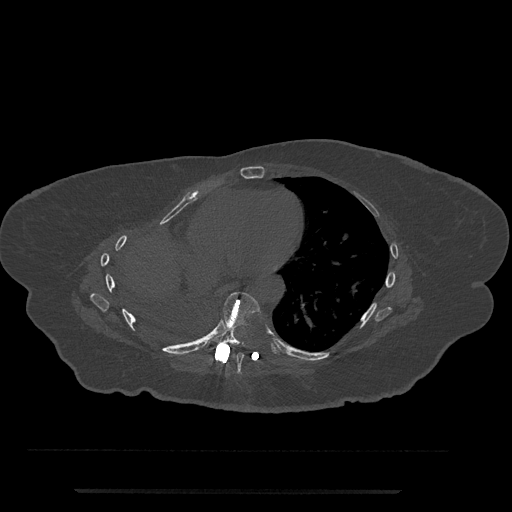
CT including the spine, one axial slice; reconstruction kernel Br40s/3; bone window (W 1800 / L 400 HU); 512 × 512 image matrix. Female patient, age 51 years. Case-level facts recorded for this patient, not image findings: primary cancer: neuro; vertebrae with lytic lesions (as recorded): T8.
Structures marked on this image (semi-automatically segmented with operator editing):
- T7 vertebra: bounding box <231,353,244,375> (left, top, right, bottom; pixels)
- T8 vertebra: <204,292,261,351>